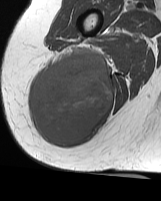
MRI of an extremity soft-tissue mass, one axial slice; slice 25 of 70 in the series (ordered by position); MR volume resampled by the dataset authors to the PET/CT grid (not the native acquisition matrix); 161 × 201 image matrix, field of view 157 × 196 mm. Female patient. Case-level facts recorded for this patient, not image findings: histological type: synovial sarcoma; grade: intermediate; site of the primary tumour: right buttock.
Outlined on this slice (expert contour drawn on MRI and transferred to this co-registered scan by the dataset authors):
- gross tumour volume including surrounding oedema: bounding box (x1, y1, x2, y2) in pixels: (31, 49, 112, 146)
- gross tumour volume (mass): (31, 49, 112, 146)